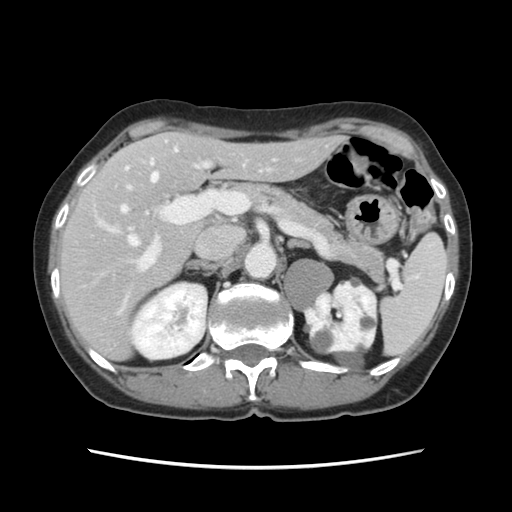
Contrast-enhanced abdominal CT, one axial slice. Position 76 of 120 along the scan axis. Intravenous contrast given. Soft-tissue window (W 400 / L 40 HU). 2.5 mm slice thickness. 512 × 512 image matrix, field of view 330 × 330 mm. Female patient, age 70 years. Case-level facts recorded for this patient, not image findings: diagnosis: colorectal cancer liver metastases, imaged before liver resection; multiple liver metastases: no; largest metastasis: 2.5 cm; chemotherapy before resection: yes.
Outlined on this slice (outlined manually by an expert reader):
- hepatic veins: bounding box (x1, y1, x2, y2) in pixels: (109, 148, 178, 246)
- liver: (60, 132, 339, 358)
- planned liver remnant (the part of the liver to remain after resection): (93, 132, 340, 285)
- portal vein (with intrahepatic branches): (119, 140, 275, 313)